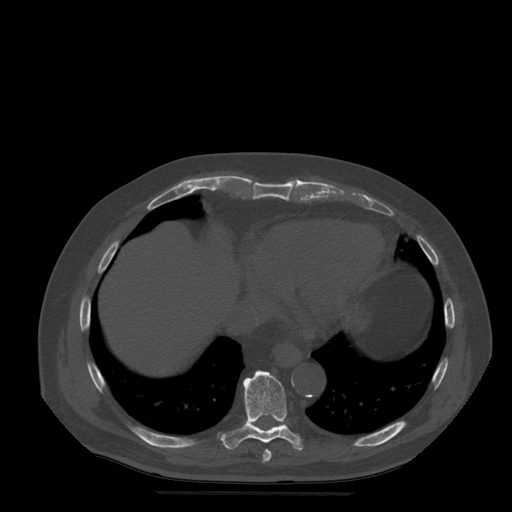
CT including the spine, one axial slice. Position 291 of 522 along the scan axis. Bone window (W 1800 / L 400 HU). 1.25 mm slice thickness. 512 × 512 image matrix. Patient age 72 years. Case-level facts recorded for this patient, not image findings: primary cancer: prostate.
Outlined on this slice (semi-automatic segmentation, software-assisted and operator-edited):
- T8 vertebra: box from (x=263, y=449) to (x=272, y=463) px
- T9 vertebra: (x=221, y=371)–(x=305, y=451)